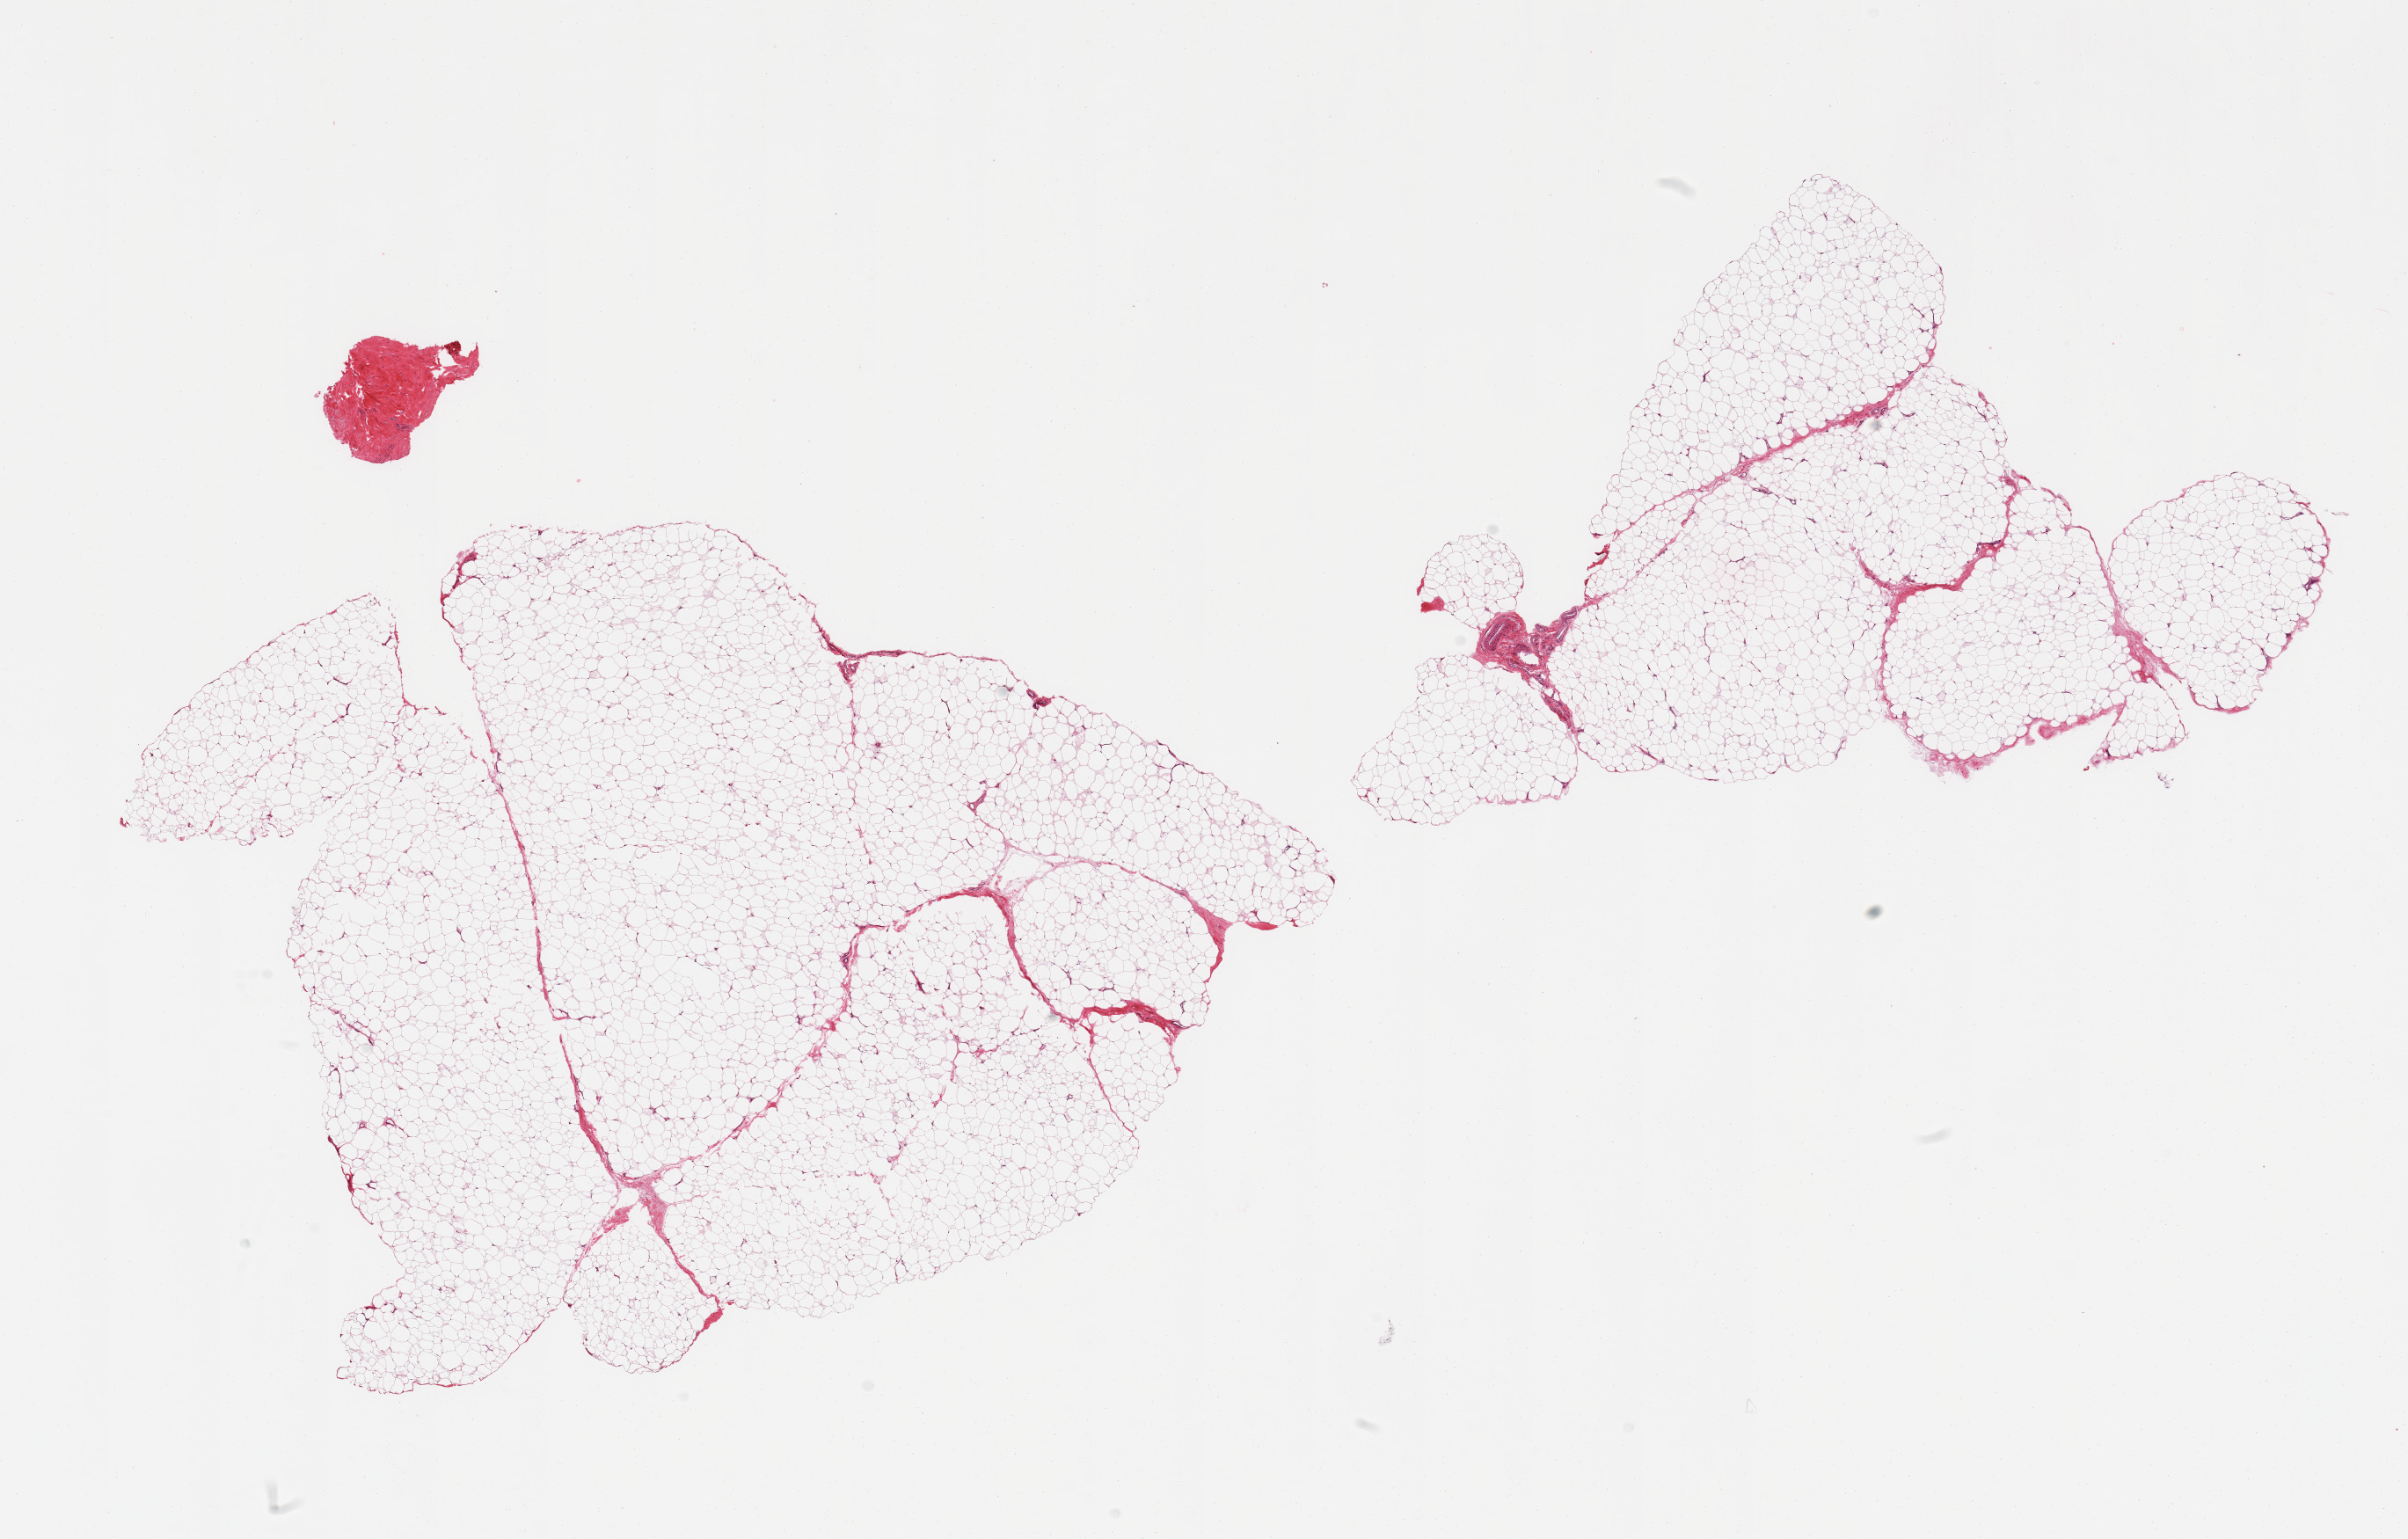
Digitized H&E-stained section — a low-resolution overview of the entire scanned area, about 21.7 x 13.8 mm (from a 20x scan), PAXgene-fixed paraffin-embedded (PFPE) section, target tissue: adipose tissue, tissue donor sample.
* review note (as recorded): 2 pieces; <5% fibrovascular content